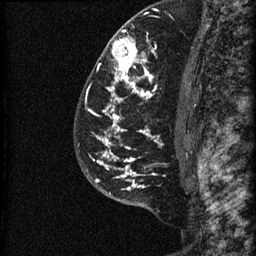
Breast MRI (dynamic contrast-enhanced), one sagittal slice. Slice 45 of 60 in the series (ordered by position). Dynamic contrast-enhanced series, image 2 of 3 at this slice position (ordered by acquisition). 1.5 T. TE 4.2 ms, TR 22.7 ms. 1.5 mm slice thickness. 256 × 256 image matrix, field of view 180 × 180 mm. Female patient, age 48 years. Case-level facts recorded for this patient, not image findings: setting: breast cancer imaged before/during neoadjuvant chemotherapy; receptor status: triple-negative.
Structures marked on this image (semi-automatically segmented with operator editing):
- analysis volume of interest (the breast-tissue region the enhancement analysis was run in; not a lesion): box from (x=81, y=23) to (x=186, y=202) px
- tumour enhancement mask (voxels above the 90 % enhancement threshold inside the analysis volume of interest): (x=89, y=30)–(x=158, y=190)